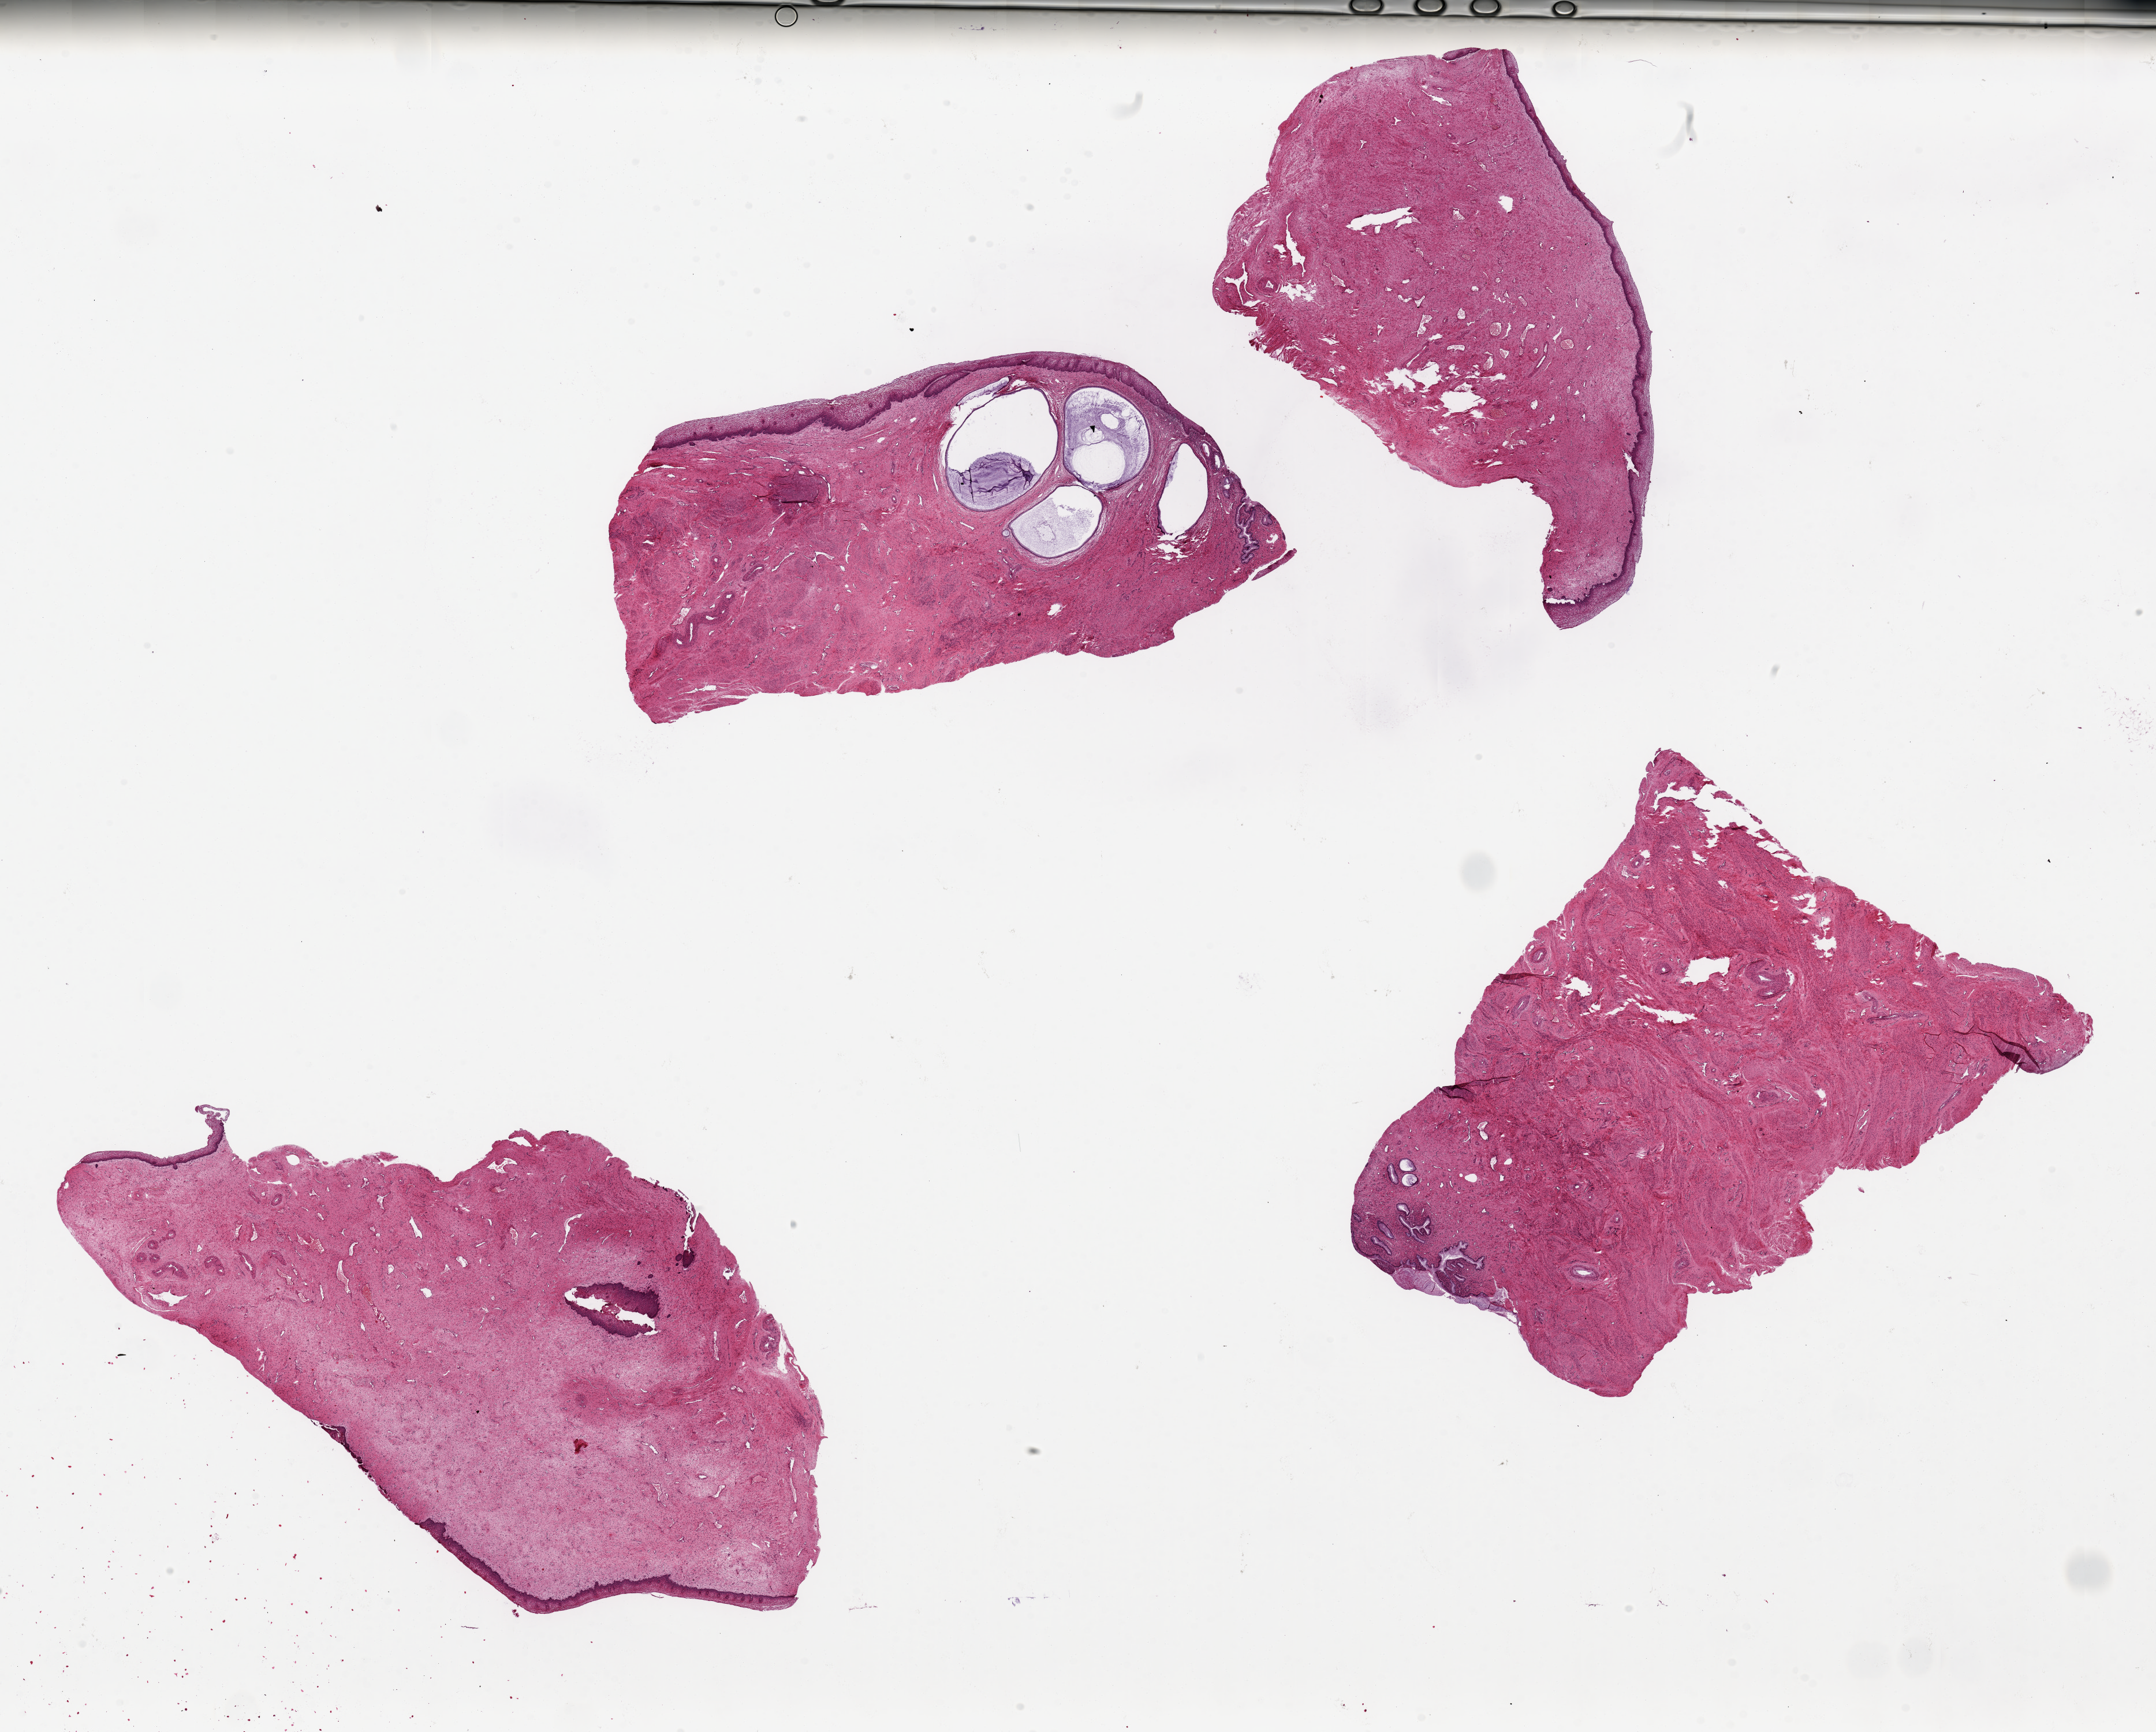
Whole-slide image, haematoxylin and eosin stain, brightfield — shown as a low-resolution overview of the whole scanned area (about 29.5 x 23.7 mm), PAXgene-fixed, paraffin-embedded tissue, target tissue: exocervix, donor tissue sample. Female donor.
Review note (as recorded): 4 pieces ~10x4mm ecto and endocervcial mucosa both (transition zone), prominentn Nabothian cysts in one, en; Where present, squamous mucosa is 5-10% of thickness.